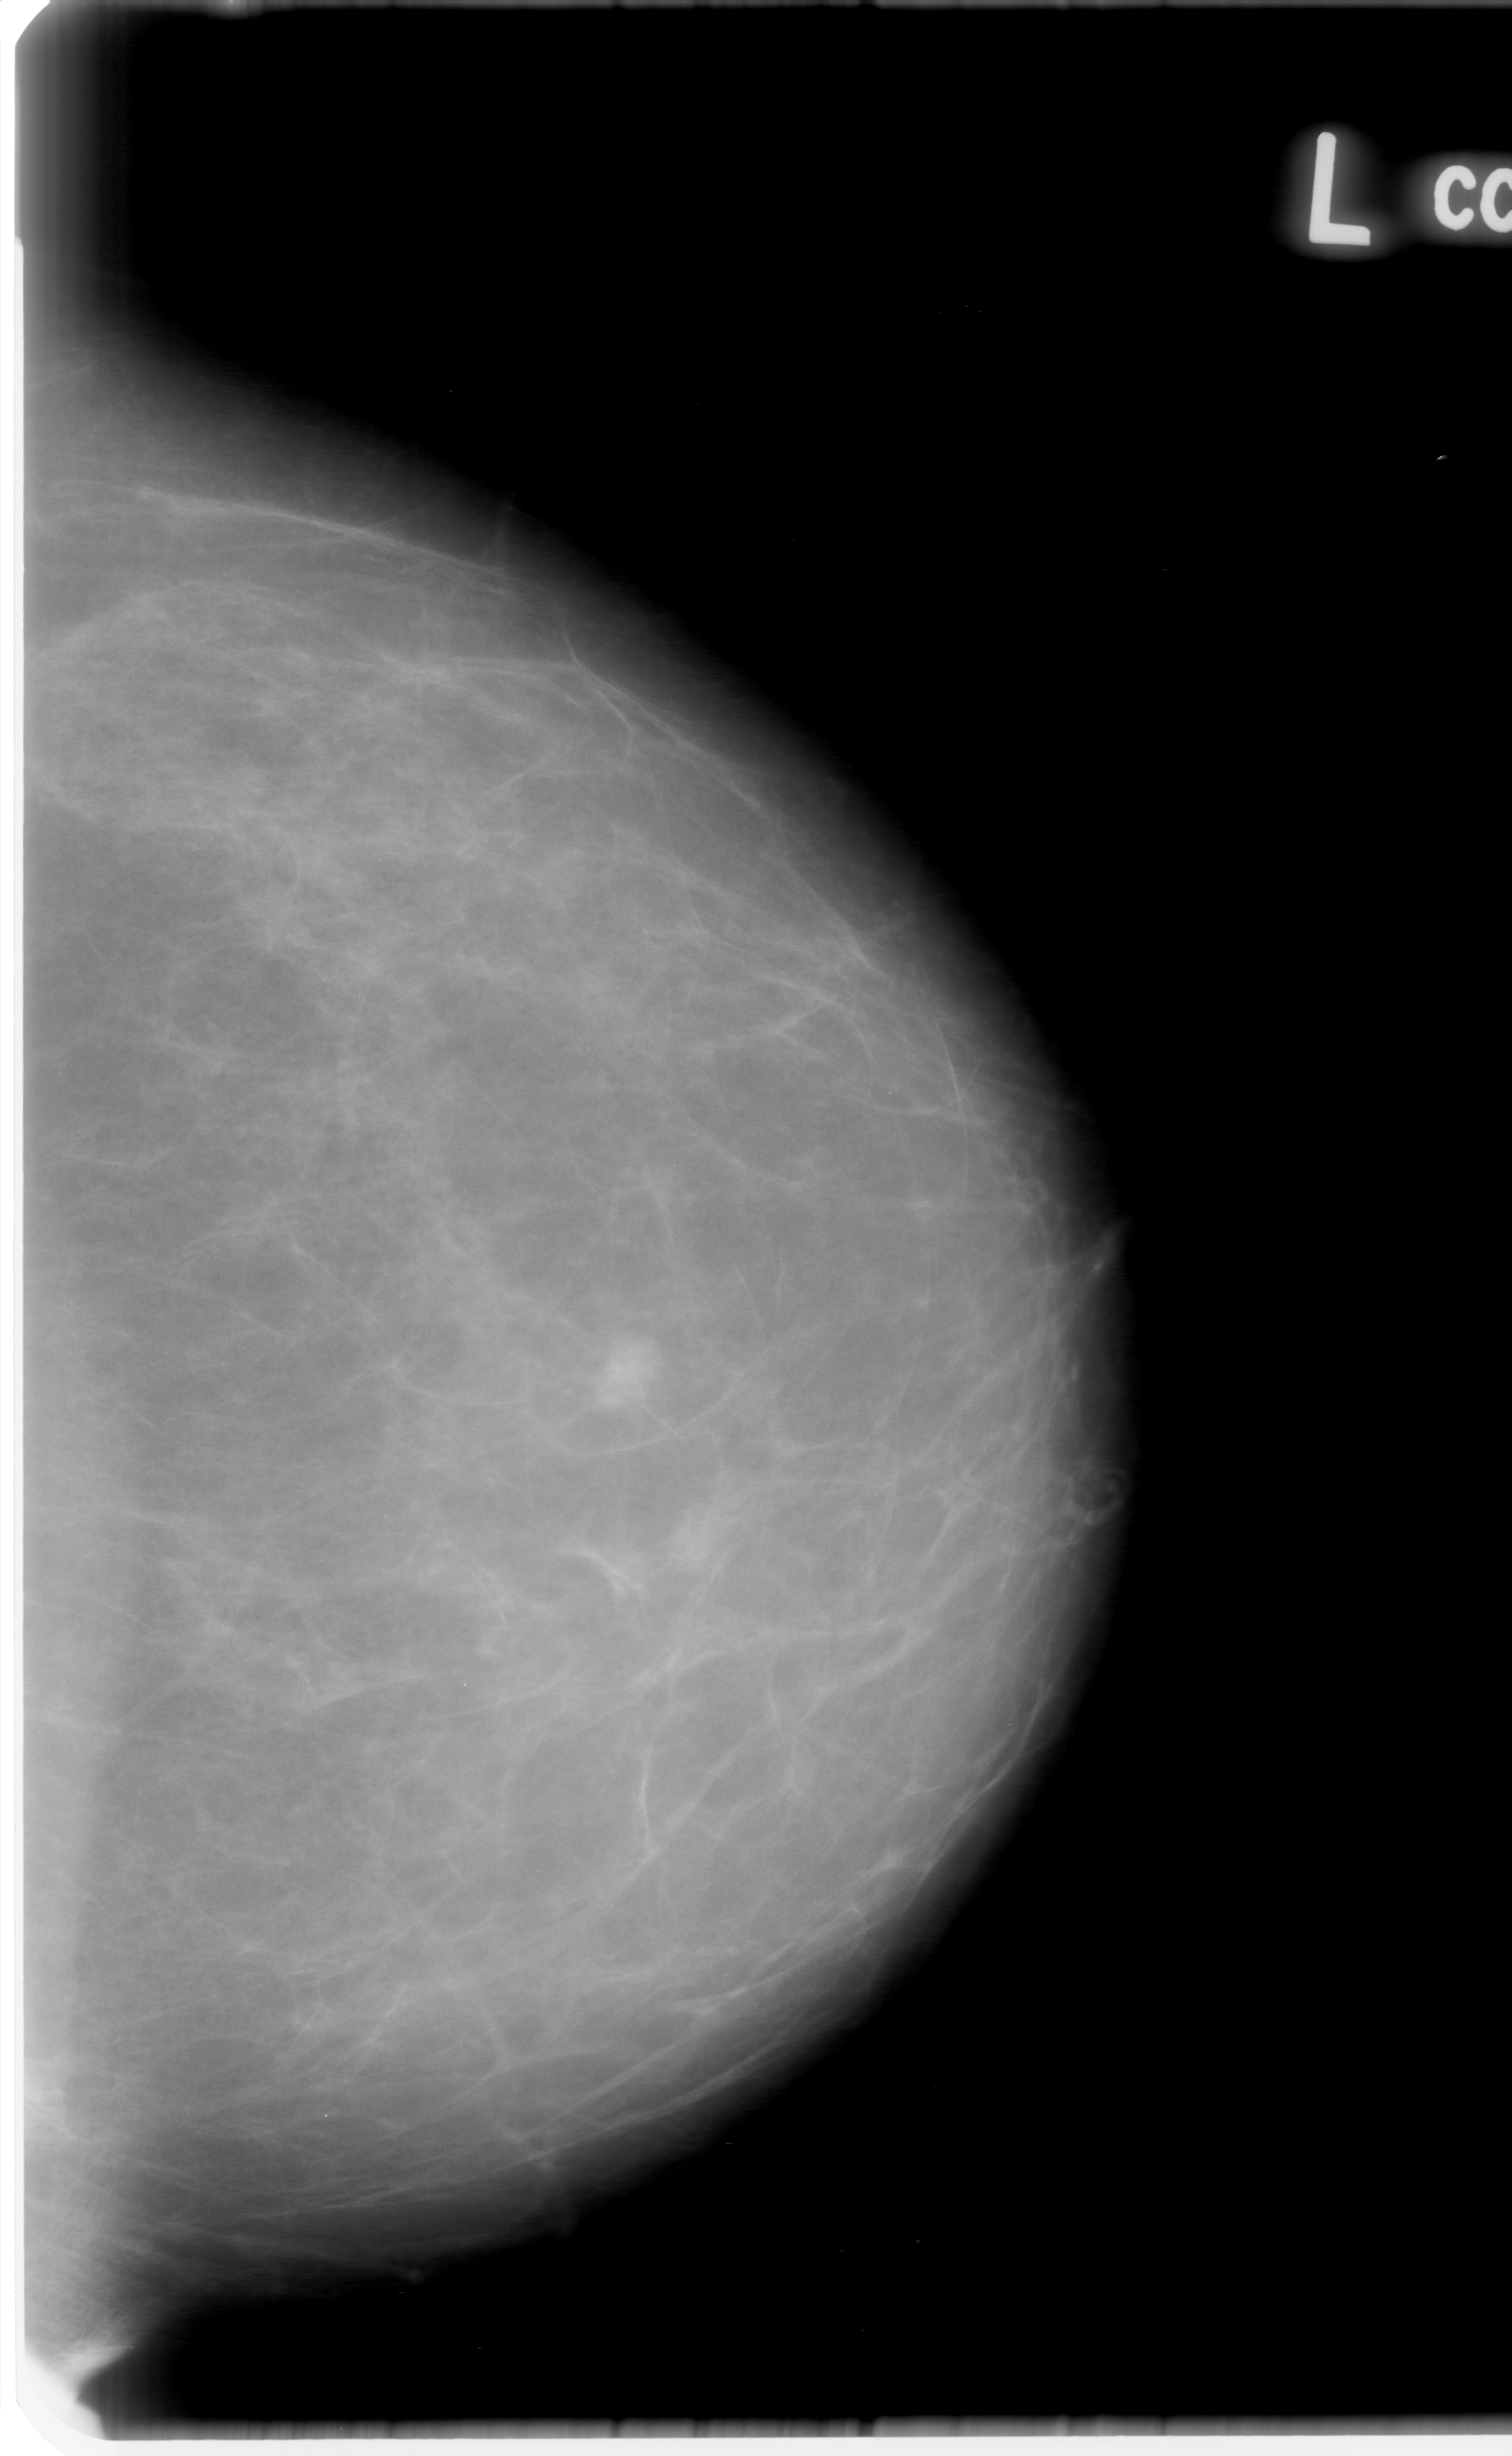
Digitized screen-film mammogram; left breast; craniocaudal (CC) view; BI-RADS breast density category 1 (scale 1–4); 1512 × 2456 image matrix.
Expert-marked regions of interest on this film, with their recorded descriptors:
- mass, shape oval, margins obscured; BI-RADS assessment category 0 (incomplete: needs additional imaging); pathology result (as recorded, not read from the image): benign: box from (x=534, y=1305) to (x=674, y=1443) px